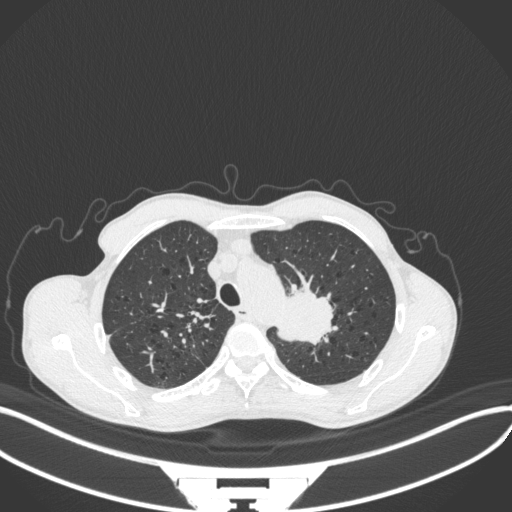
Chest CT, one axial slice. Slice 332 of 394 in the series (ordered by position). Reconstruction kernel B31f. Lung window (W 1500 / L -600 HU). 1 mm slice thickness. 512 × 512 image matrix, field of view 400 × 400 mm. Patient: male, 65 years. Case-level facts recorded for this patient, not image findings: clinical TNM (as recorded): T2b N0 M0; histopathological grade: G2.
Outlined on this slice (bounding box drawn by a radiologist):
- lung tumour (recorded histology: adenocarcinoma): bounding box (x1, y1, x2, y2) in pixels: (273, 276, 339, 343)